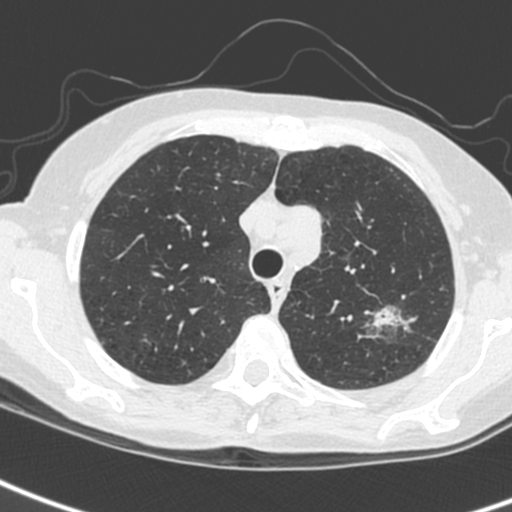
Low-dose screening chest CT, one axial slice; position 200 of 242 along the scan axis; 120 kVp; lung window (W 1500 / L -600 HU); 1.3 mm slice thickness; 512 × 512 image matrix, field of view 284 × 284 mm.
Outlined on this slice (expert manual segmentation):
- lesion 1 (tumor, upper lobe of left lung): box from (x=373, y=308) to (x=397, y=329) px
- lesion 3 (tumor, upper lobe of left lung): (x=296, y=205)–(x=322, y=262)